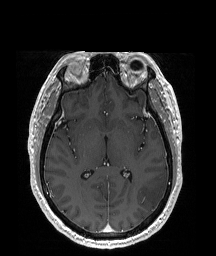
Brain MRI from a brain-tumour surgery series, one axial slice; position 100 of 192 along the scan axis; T1-weighted post-contrast; 216 × 256 image matrix, field of view 219 × 260 mm. Case-level facts recorded for this patient, not image findings: histopathology: Glioblastoma; WHO grade: 4; IDH mutation: no.
Outlined on this slice (manually delineated by an expert):
- tumour: bounding box (x1, y1, x2, y2) in pixels: (140, 173, 168, 207)